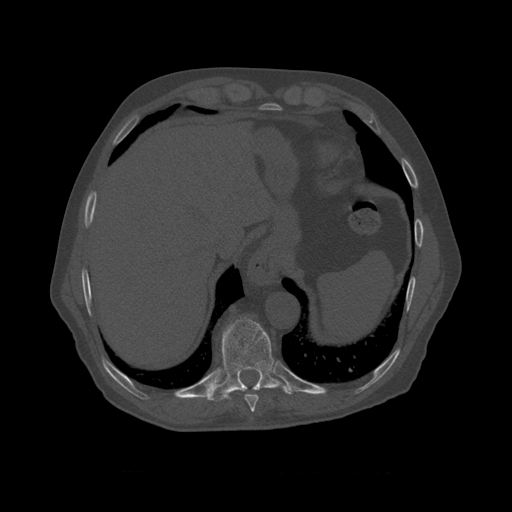
CT including the spine, one axial slice; position 431 of 450 along the scan axis; reconstruction kernel STANDARD; bone window (W 1800 / L 400 HU); 1.25 mm slice thickness; 512 × 512 image matrix. Patient age 75 years. Case-level facts recorded for this patient, not image findings: primary cancer: prostate.
Structures marked on this image (semi-automatic segmentation, software-assisted and operator-edited):
- T8 vertebra: bounding box <245,390,259,410> (left, top, right, bottom; pixels)
- T9 vertebra: <215,317,291,400>